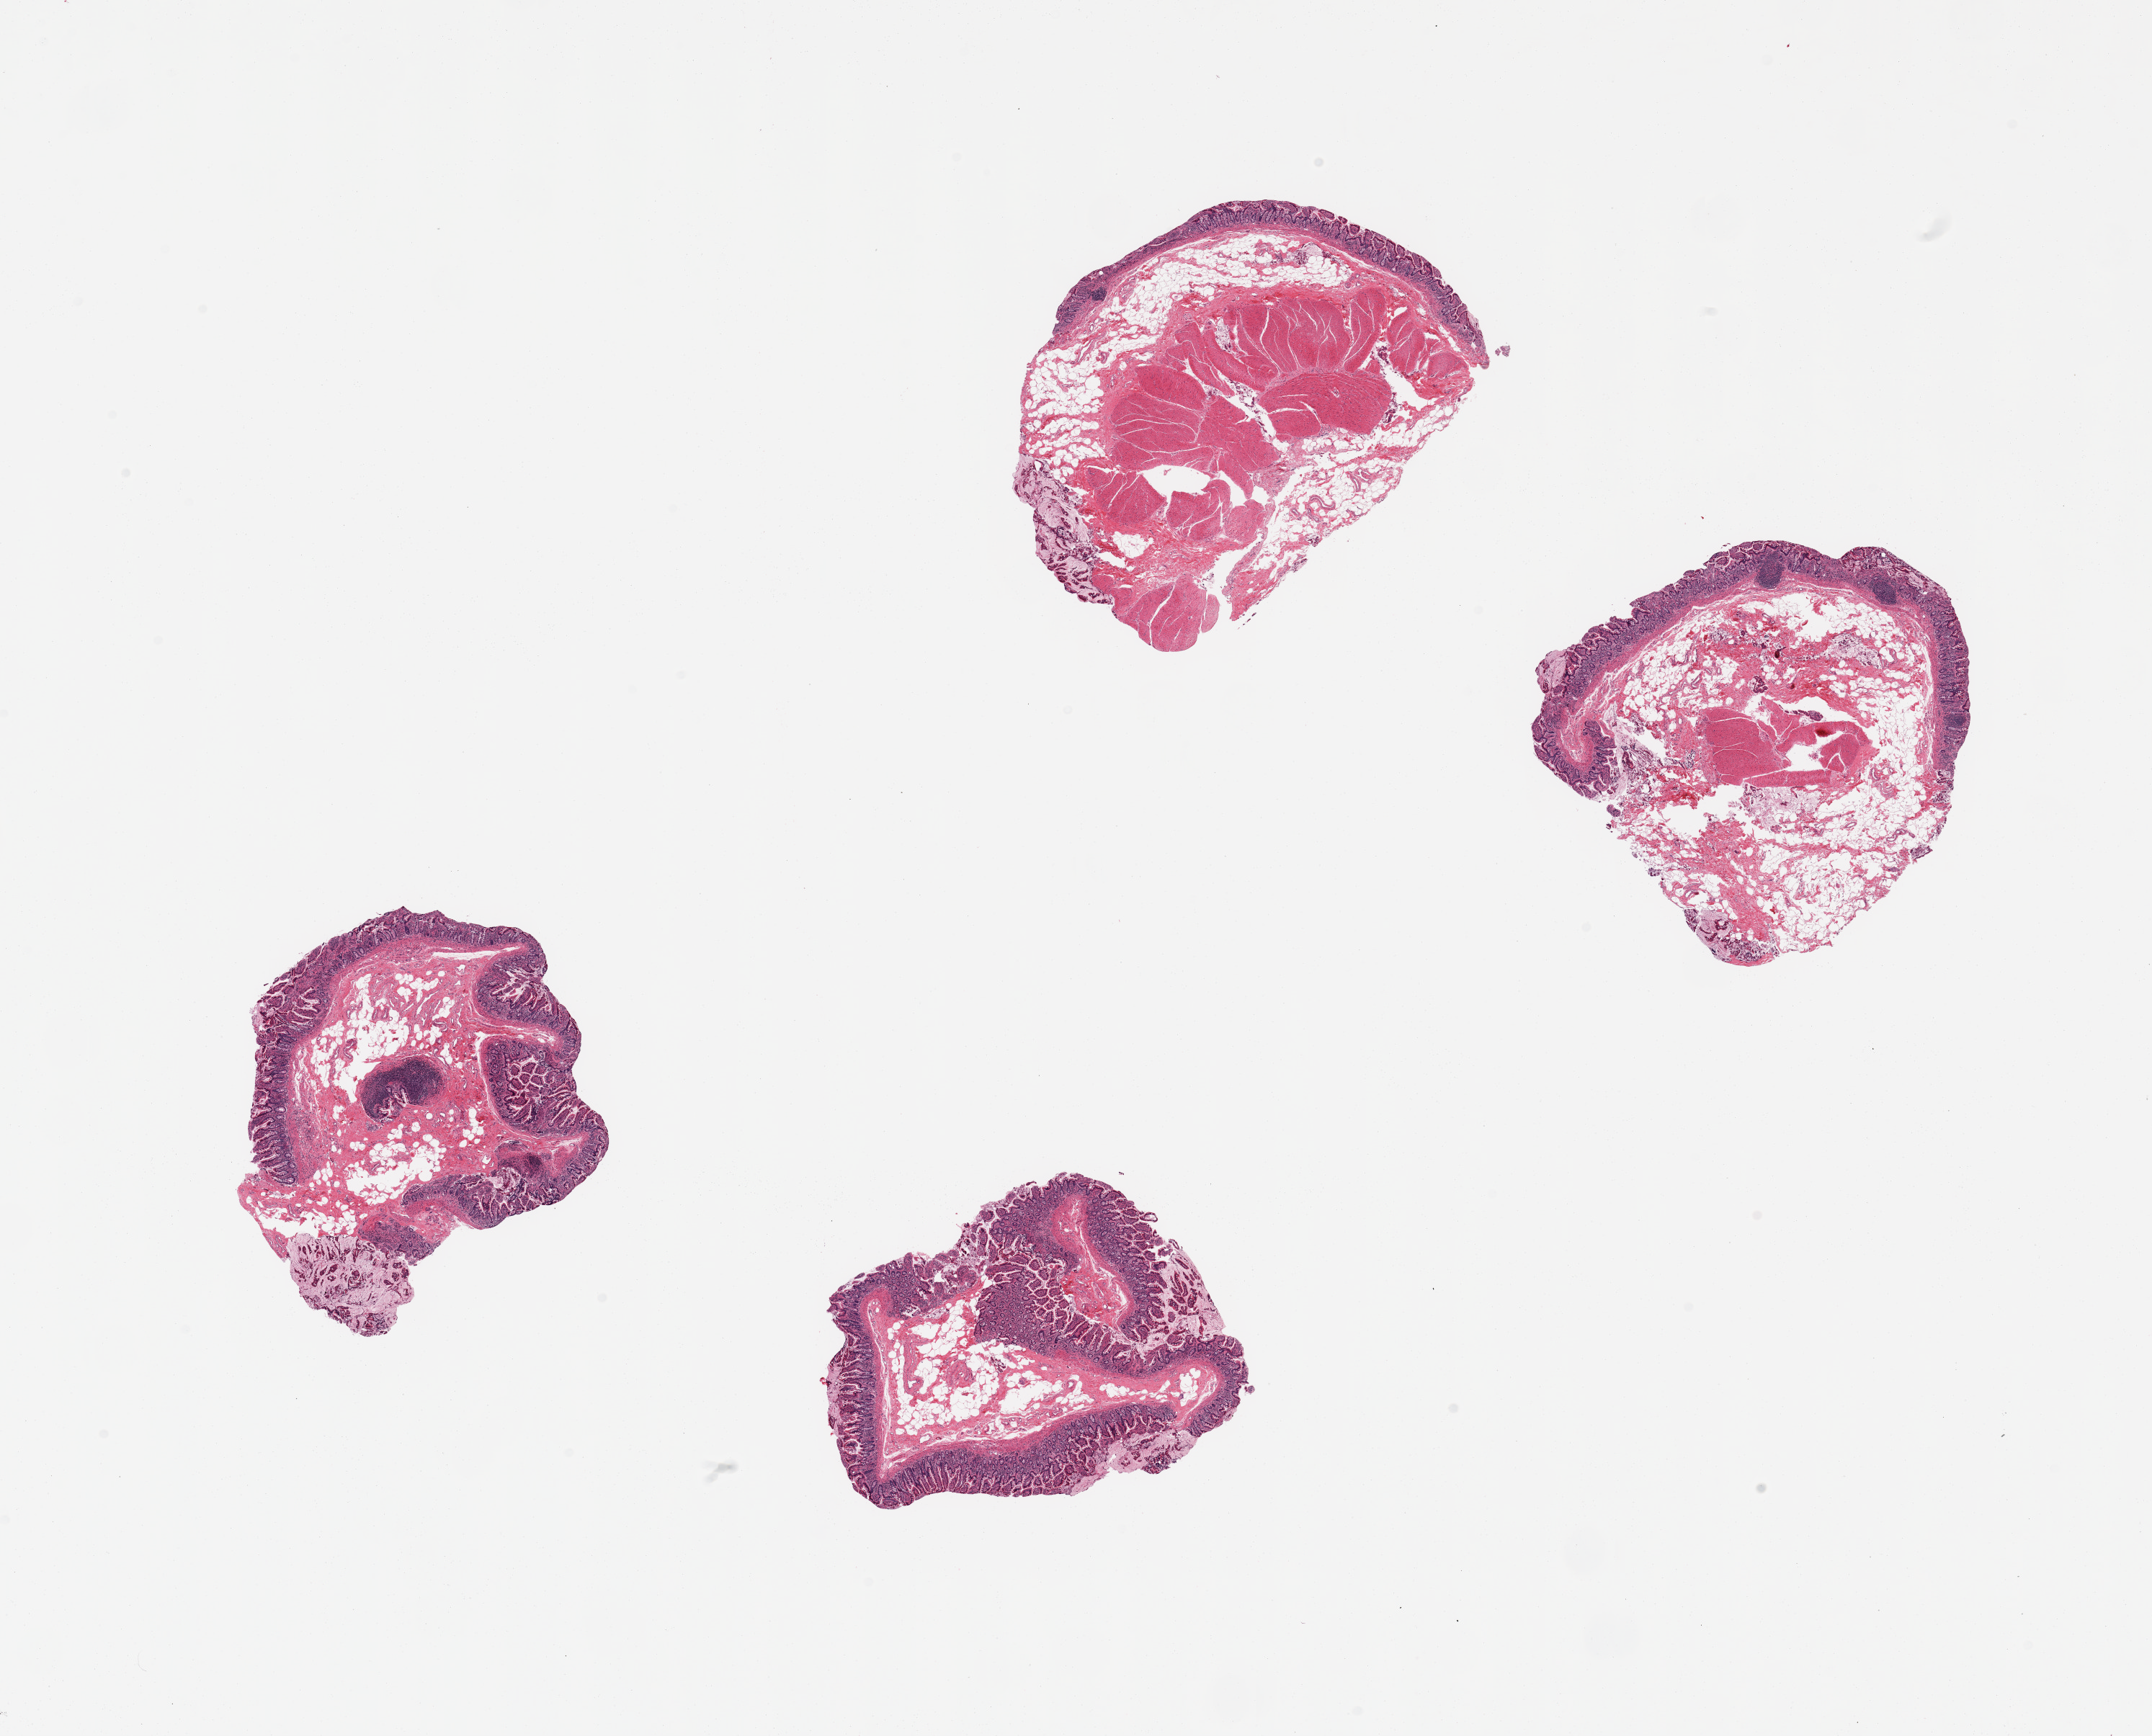
Whole-slide image, H&E stain, shown as a low-resolution overview of the whole scanned area (about 23.6 x 19.1 mm). PAXgene-fixed, paraffin-embedded tissue. Target tissue: ileum. Tissue donor sample. Donor sex: male.
Reviewer comment on this tissue sample: 4 pieces; several lymphoid nodules in well preserved mucosa.